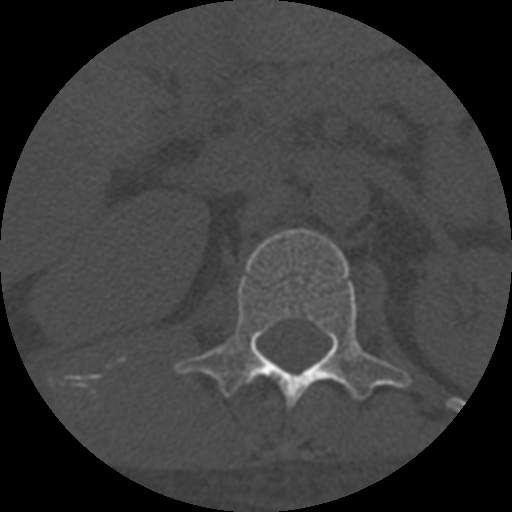
CT including the spine, one axial slice; slice 290 of 708 in the series (ordered by position); 120 kVp; one of 3 acquisitions stored at this slice position; bone window (W 1800 / L 400 HU); 512 × 512 image matrix, field of view 160 × 160 mm. Patient age 55 years. Case-level facts recorded for this patient, not image findings: primary cancer: colon; vertebrae with lytic lesions (as recorded): T12, L1, L5.
Structures marked on this image (semi-automatically segmented with operator editing):
- L1 vertebra: bounding box <175,229,412,407> (left, top, right, bottom; pixels)